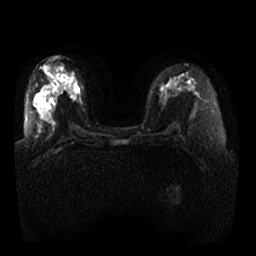
Breast MRI, one axial slice; position 12 of 25 along the scan axis; diffusion-weighted series; image 2 of 4 stored at this slice position (different b-values; order by instance number); 1.5 T; 4 mm slice thickness; 256 × 256 image matrix, field of view 350 × 350 mm. Female patient.
Annotated regions visible in this slice (outlined manually by an expert reader):
- tumour on diffusion-weighted imaging: bounding box [x1, y1, x2, y2] px = [72, 84, 79, 97]